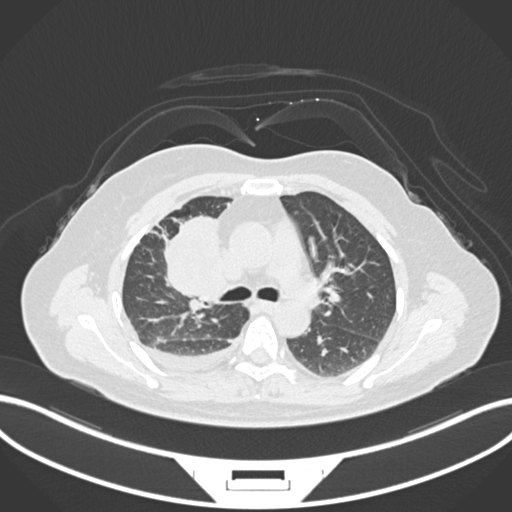
Chest CT, one axial slice. Slice 95 of 172 in the series (ordered by position). Lung window (W 1500 / L -600 HU). 1 mm slice thickness. 512 × 512 image matrix, field of view 400 × 400 mm. Patient: female, 52 years. From the clinical record (not read from this slice): clinical TNM (as recorded): T3 N1 M1.
Structures marked on this image (bounding box drawn by a radiologist):
- lung tumour (recorded histology: adenocarcinoma): box from (x=155, y=207) to (x=219, y=307) px